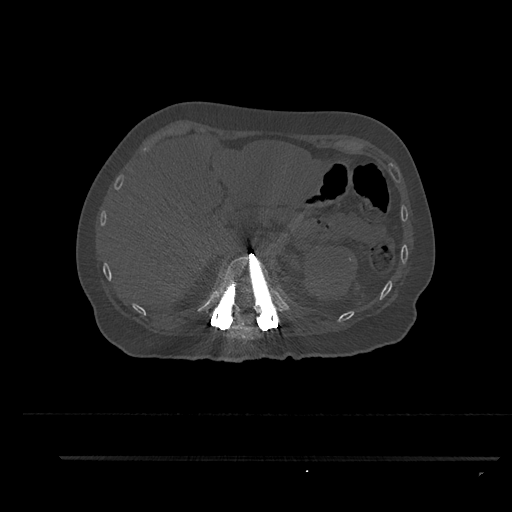
CT including the spine, one axial slice. Reconstruction kernel Br40s/3. 120 kVp. Bone window (W 1800 / L 400 HU). 0.5 mm slice thickness. 512 × 512 image matrix, field of view 408 × 408 mm. Patient: female, 44 years. From the clinical record (not read from this slice): primary cancer: renal; vertebrae with lytic lesions (as recorded): L1.
Annotated regions visible in this slice (semi-automatic segmentation, software-assisted and operator-edited):
- T11 vertebra: bounding box <232,322,243,329> (left, top, right, bottom; pixels)
- T12 vertebra: <213,254,283,320>